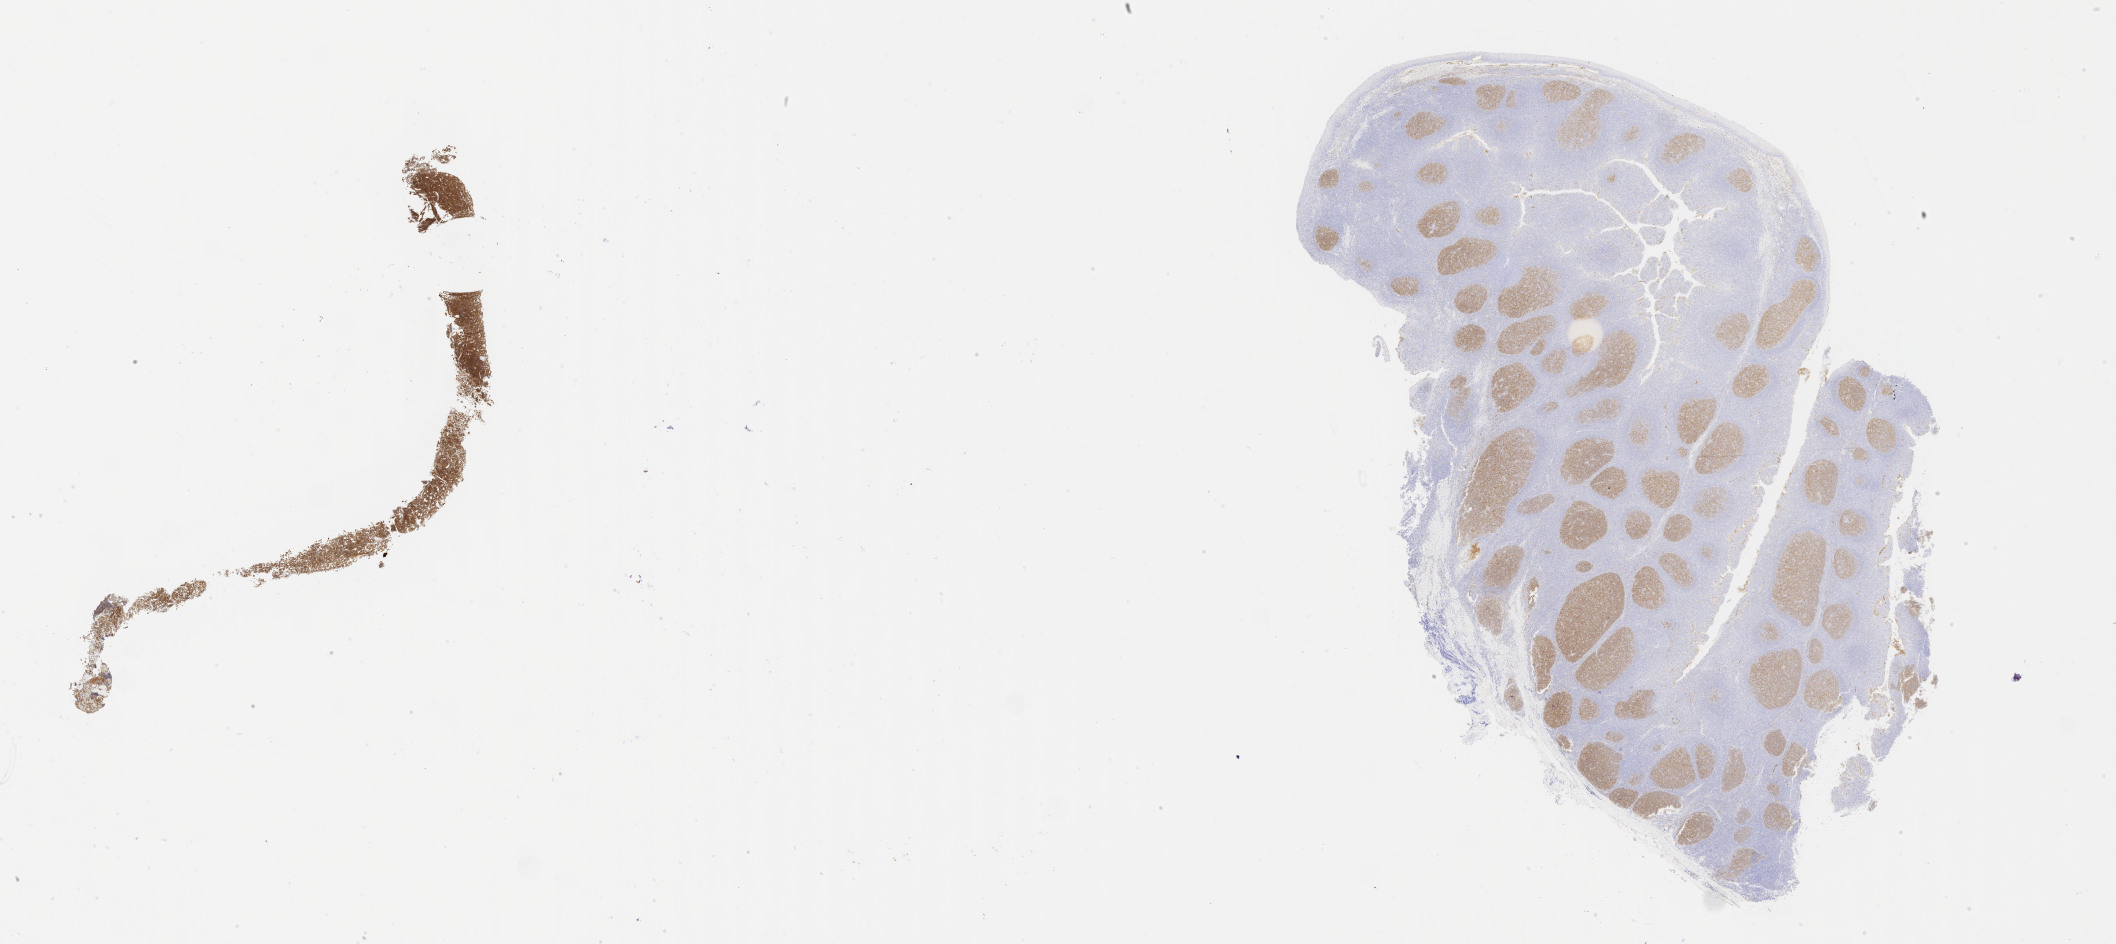
Immunohistochemistry (IHC) whole-slide image stained for CD10, a low-resolution overview of the entire scanned area, about 34.2 x 15.3 mm, tumor tissue, anatomic site: ovary. Female patient; age at initial diagnosis 7 years.
- histologic diagnosis: Burkitt lymphoma, NOS